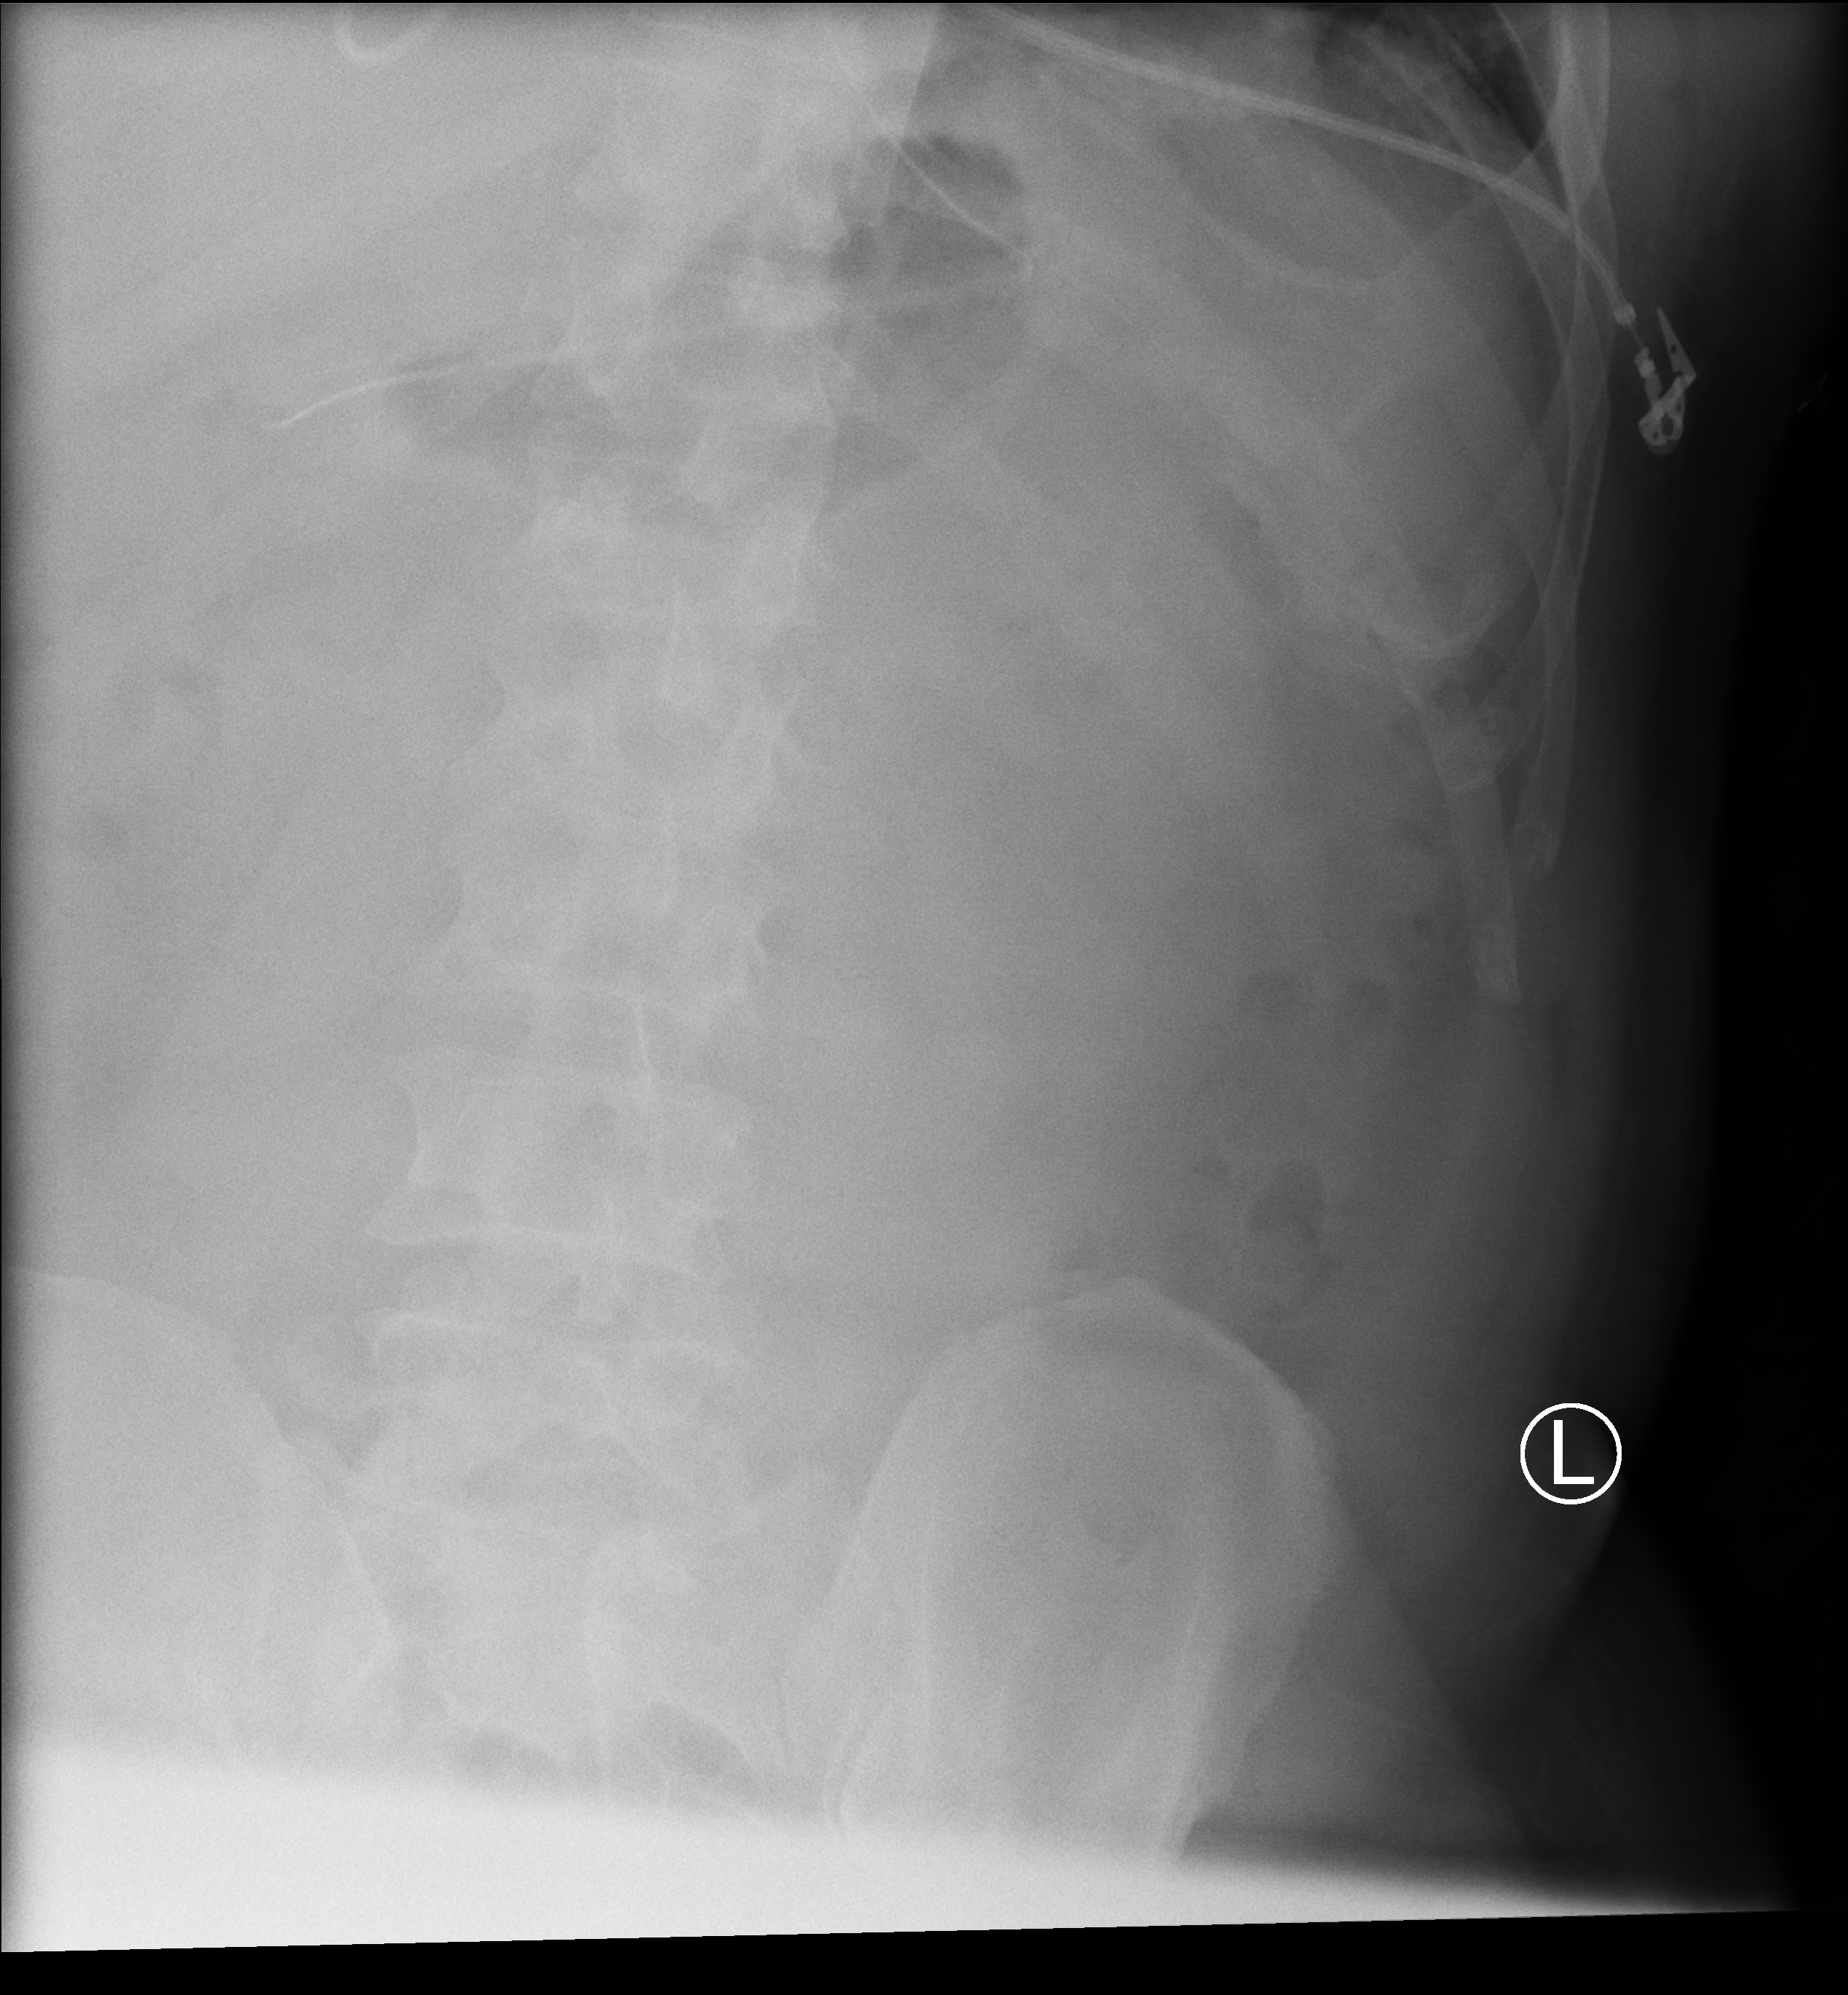
Portable abdomen radiograph; anteroposterior (AP) projection. Patient hospitalised with COVID-19; male, aged 18–59 years.
From the hospital-stay record, not from the radiograph (when in the stay this image was taken is not recorded): admitted to intensive care during this hospital stay: no.